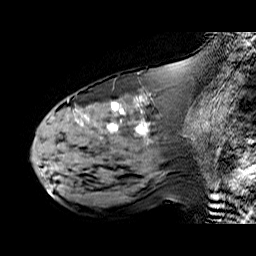
Breast MRI (dynamic contrast-enhanced), one sagittal slice. Slice 28 of 60 in the series (ordered by position). Dynamic contrast-enhanced series, time point 2 of 6 at this slice position (early post-contrast). 1.5 T. TE 6.3 ms, TR 32.9 ms. 4 mm slice thickness. 256 × 256 image matrix, field of view 200 × 200 mm. Female patient. Case-level facts recorded for this patient, not image findings: setting: breast cancer imaged before/during neoadjuvant chemotherapy; receptor status: HER2-positive.
Structures marked on this image (semi-automatically segmented with operator editing):
- analysis volume of interest (the breast-tissue region the enhancement analysis was run in; not a lesion): bounding box <48,92,195,174> (left, top, right, bottom; pixels)
- tumour enhancement mask (voxels above the 100 % enhancement threshold inside the analysis volume of interest): <81,97,144,131>